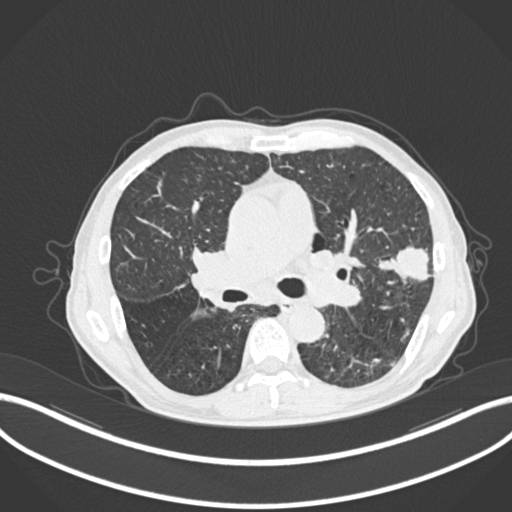
Chest CT, one axial slice; position 142 of 287 along the scan axis; reconstruction kernel B30f; lung window (W 1500 / L -600 HU); 1 mm slice thickness; 512 × 512 image matrix, field of view 400 × 400 mm. Patient: male, 74 years. From the clinical record (not read from this slice): clinical TNM (as recorded): T2a N1 M0.
Structures marked on this image (bounding box drawn by a radiologist):
- lung tumour (recorded histology: adenocarcinoma): bounding box (x1, y1, x2, y2) in pixels: (379, 246, 434, 286)